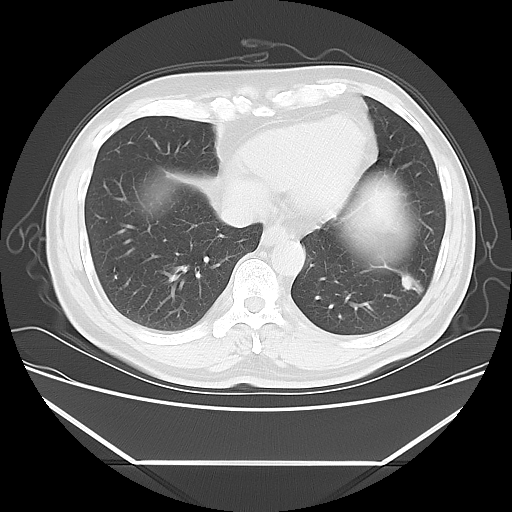
Chest CT, one axial slice. Position 18 of 57 along the scan axis. Reconstruction kernel LUNG. 120 kVp. Lung window (W 1500 / L -600 HU). 5 mm slice thickness. 512 × 512 image matrix, field of view 384 × 384 mm. Male patient, age 53 years. From the clinical record (not read from this slice): clinical TNM (as recorded): T1c N0 M0.
Annotated regions visible in this slice (rectangle marked by the reading radiologist):
- lung tumour (recorded histology: adenocarcinoma): bounding box <398,270,427,289> (left, top, right, bottom; pixels)